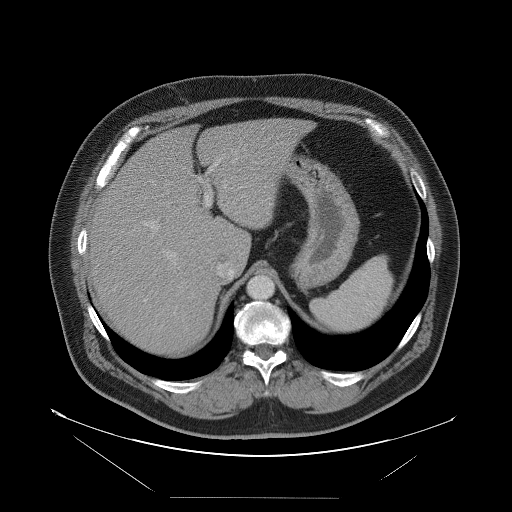
Contrast-enhanced abdominal CT, one axial slice; position 72 of 114 along the scan axis; 120 kVp; intravenous contrast given; soft-tissue window (W 400 / L 40 HU); 512 × 512 image matrix. Male patient, age 61 years. Case-level facts recorded for this patient, not image findings: diagnosis: colorectal cancer liver metastases, imaged before liver resection; multiple liver metastases: no.
Outlined on this slice (manually delineated by an expert):
- hepatic veins: bounding box <151,181,235,284> (left, top, right, bottom; pixels)
- liver: <89,119,307,354>
- planned liver remnant (the part of the liver to remain after resection): <146,119,306,265>
- portal vein (with intrahepatic branches): <141,150,237,302>